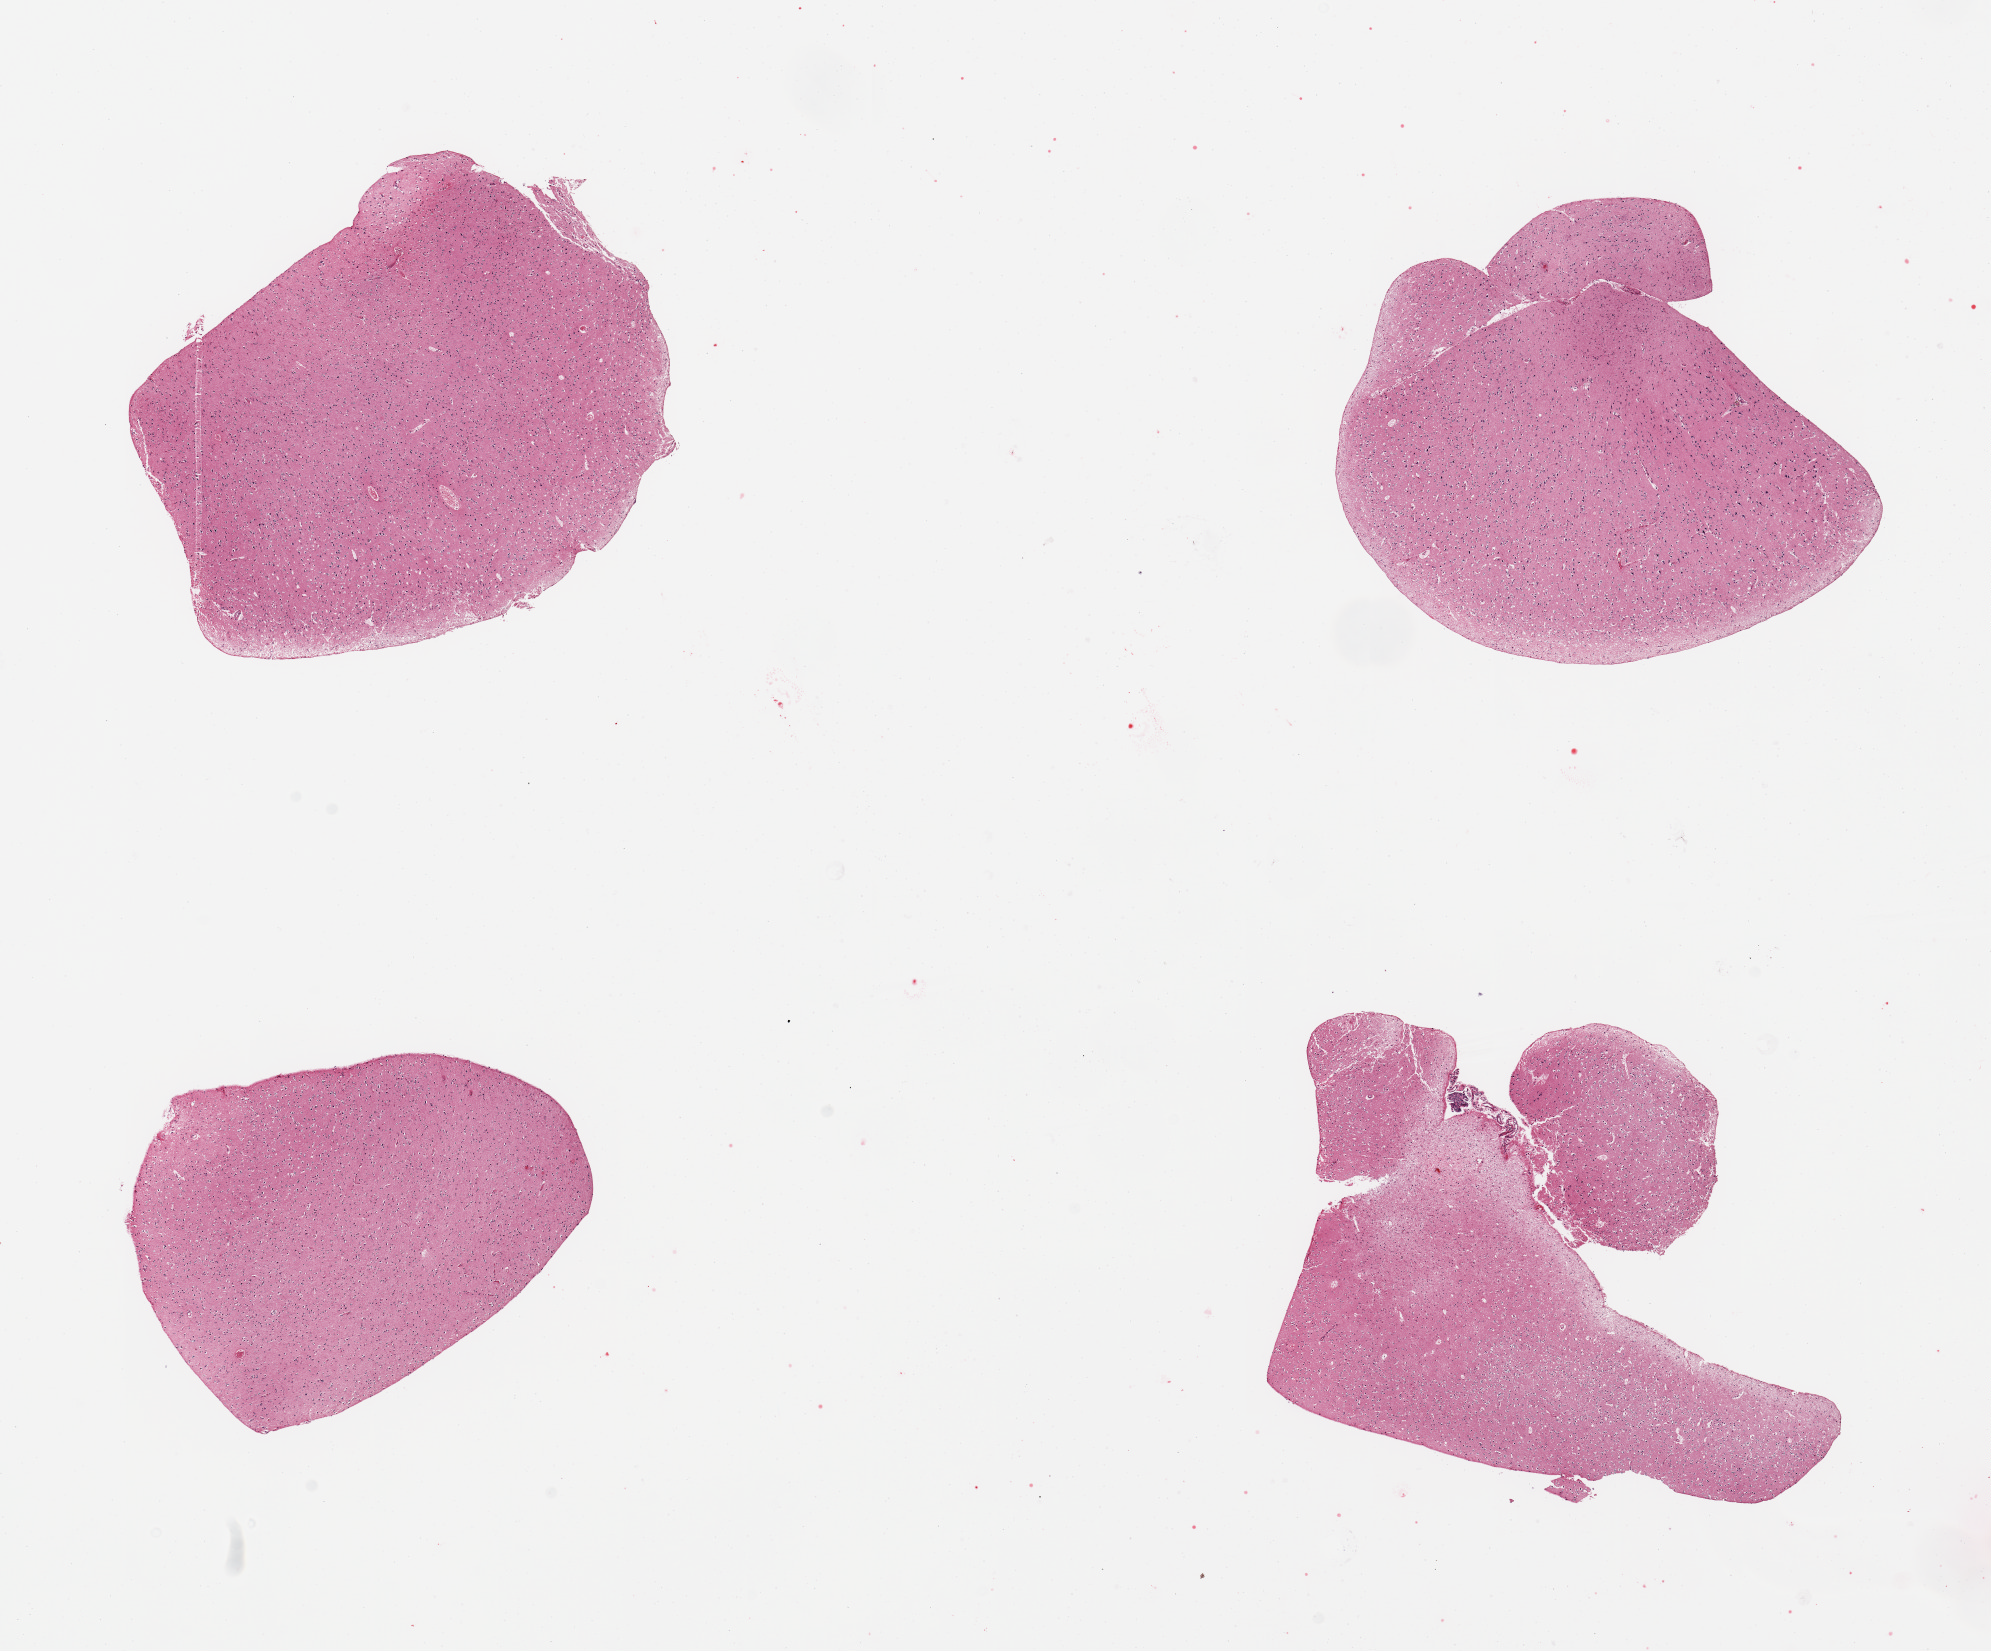
H&E whole-slide image, brightfield, a low-resolution overview of the entire scanned area, about 15.8 x 13.1 mm (slide scanned at 20x). PAXgene-fixed, paraffin-embedded tissue. Sampled site (target tissue): cerebral cortex. Tissue donor sample. Male donor.
Review note (as recorded): 4 pieces; small fragment of meninges.